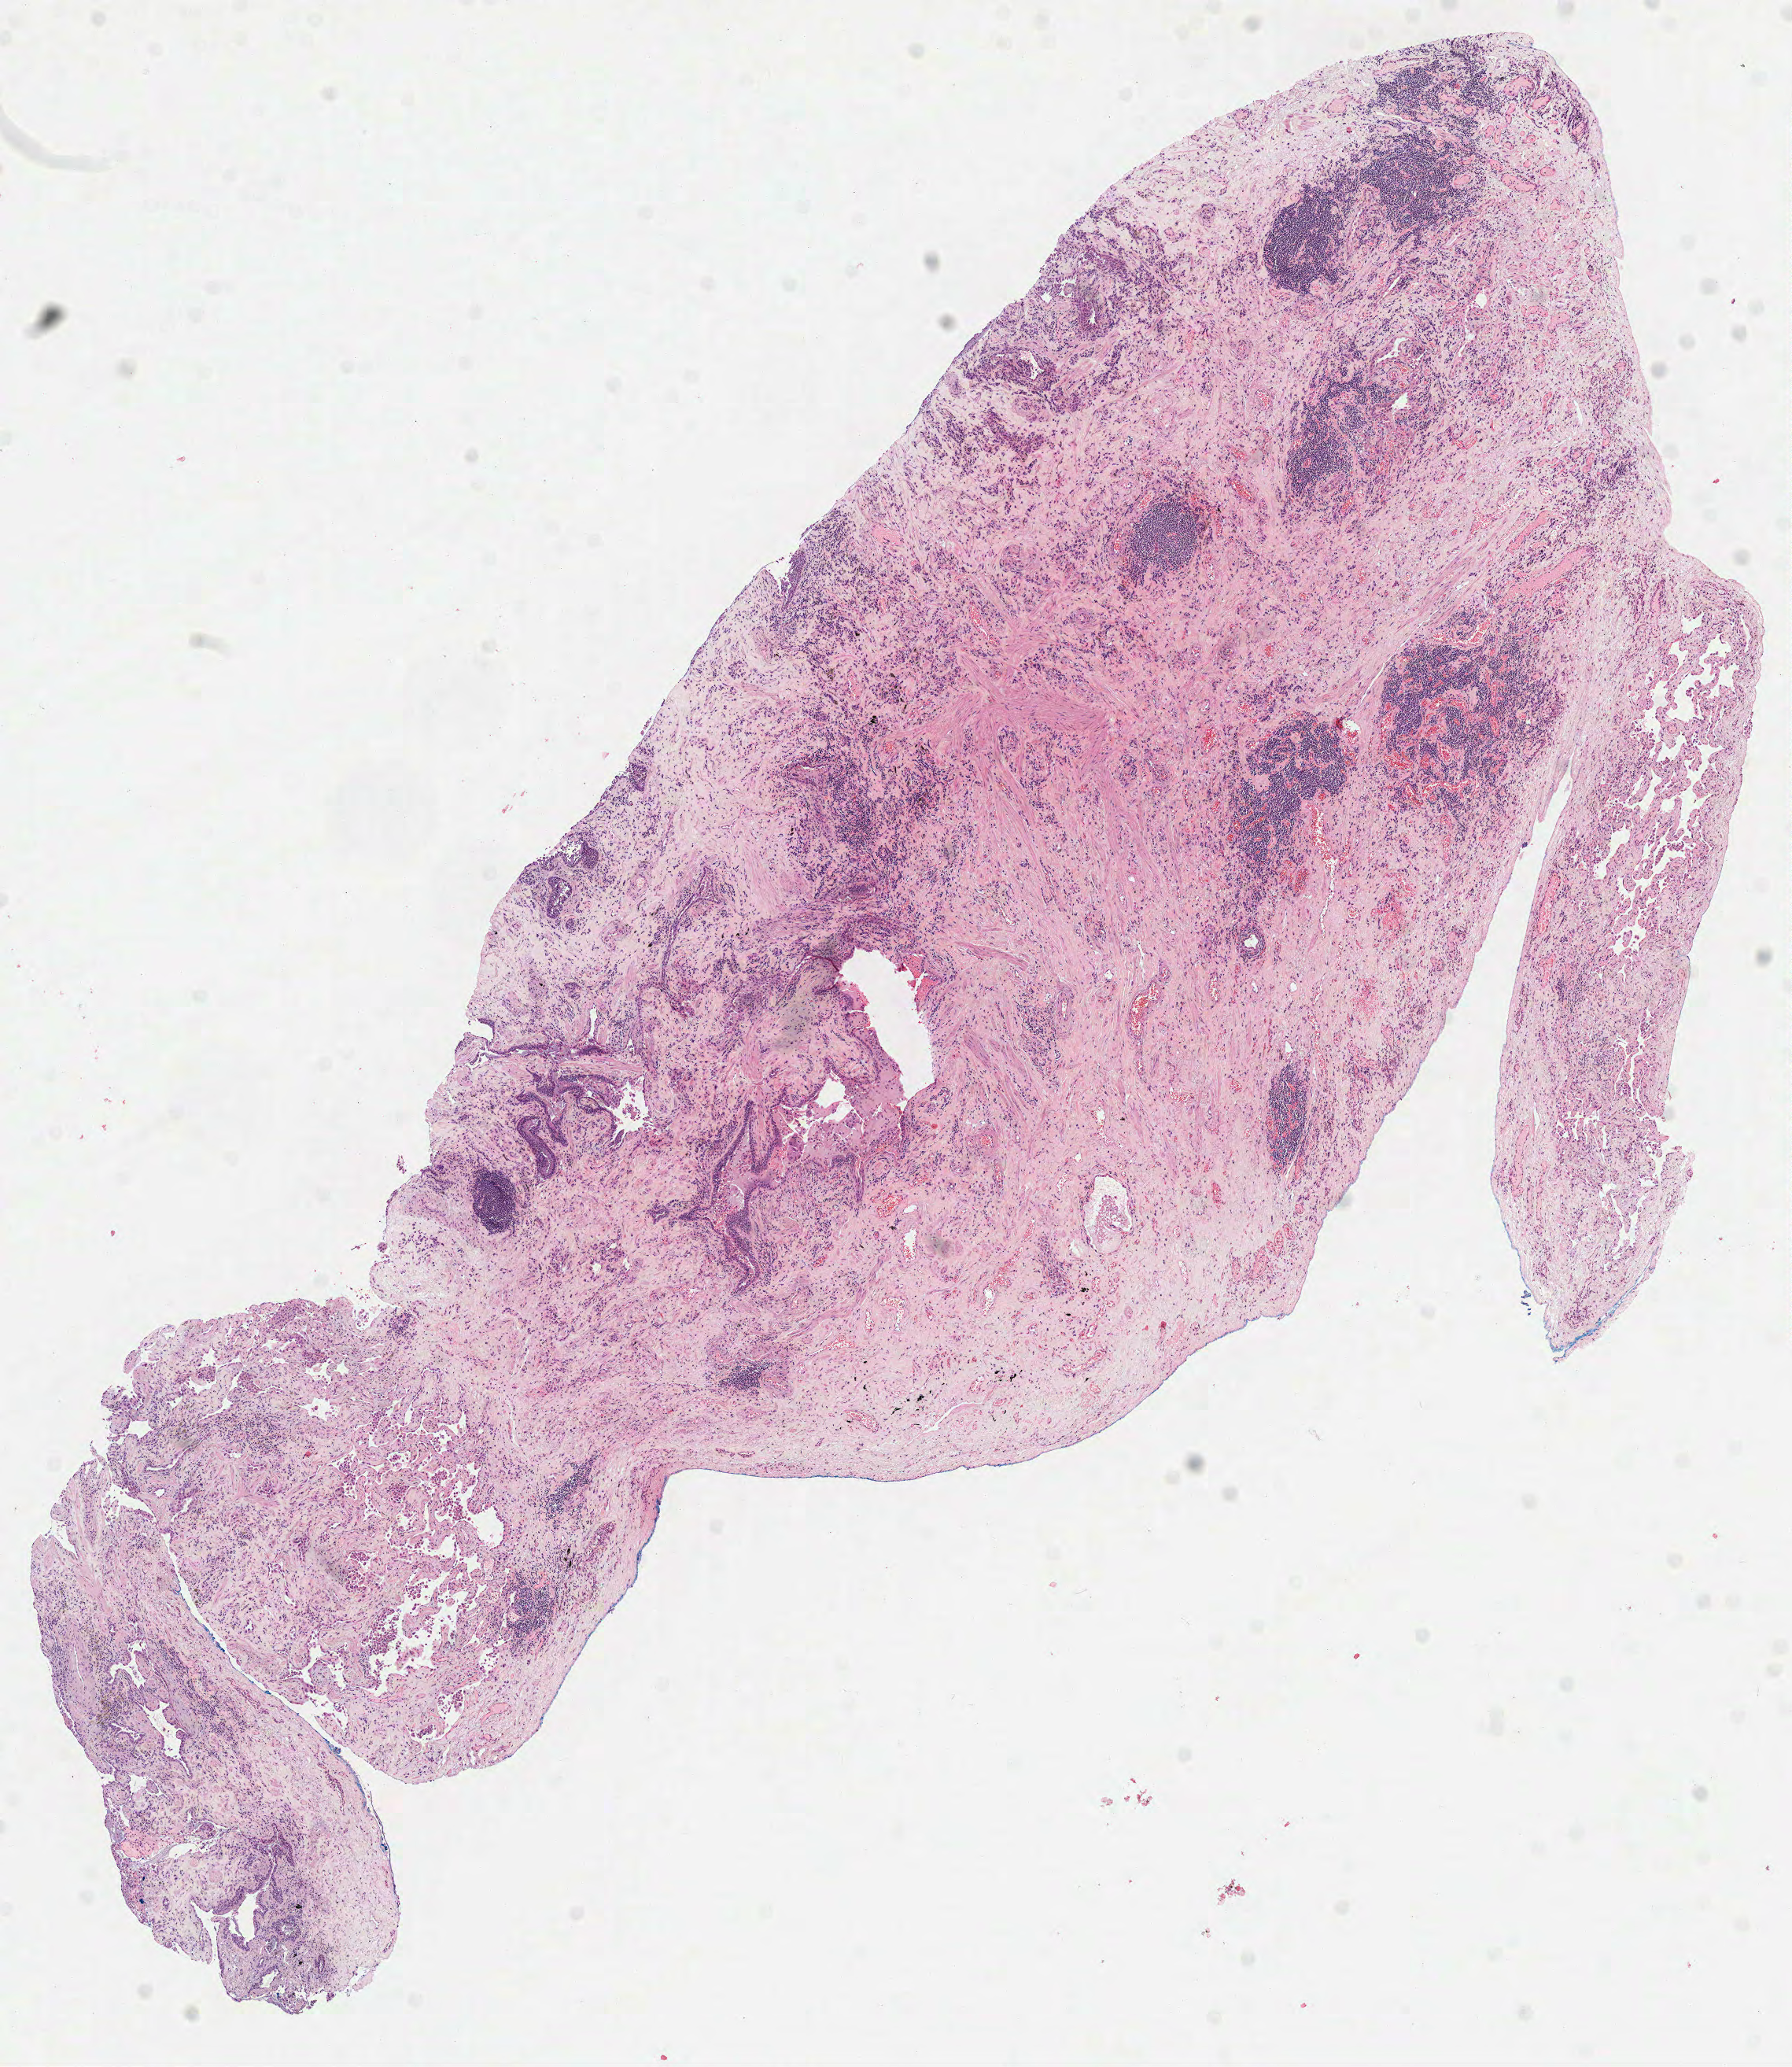
Digitized H&E tissue section (whole slide) — whole scanned area (about 9.2 x 10.6 mm, slide scanned at 40x) shown as a low-resolution overview; frozen section from the top of the tissue portion; solid tissue normal (non-tumour tissue) sample from the lung. Female patient; age at initial diagnosis 66 years. Inflammatory infiltration, as recorded: lymphocyte infiltration 35%, monocyte infiltration 0%, neutrophil infiltration 0%.
This section: solid tissue normal (non-tumour) sample from the same patient. Patient diagnosis: Squamous cell carcinoma, NOS (upper lobe, lung).